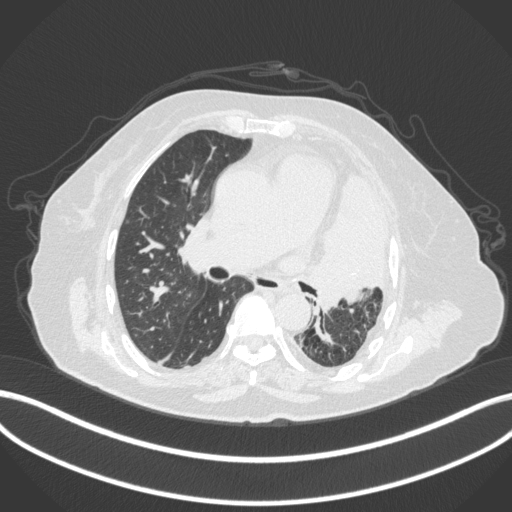
Chest CT, one axial slice. Position 215 of 399 along the scan axis. Reconstruction kernel B31f. 120 kVp. Lung window (W 1500 / L -600 HU). 512 × 512 image matrix, field of view 400 × 400 mm. Female patient, age 75 years. Case-level facts recorded for this patient, not image findings: clinical TNM (as recorded): T3 N3 M1.
Annotated regions visible in this slice (rectangle marked by the reading radiologist):
- lung tumour (recorded histology: adenocarcinoma): bounding box <306,168,389,314> (left, top, right, bottom; pixels)